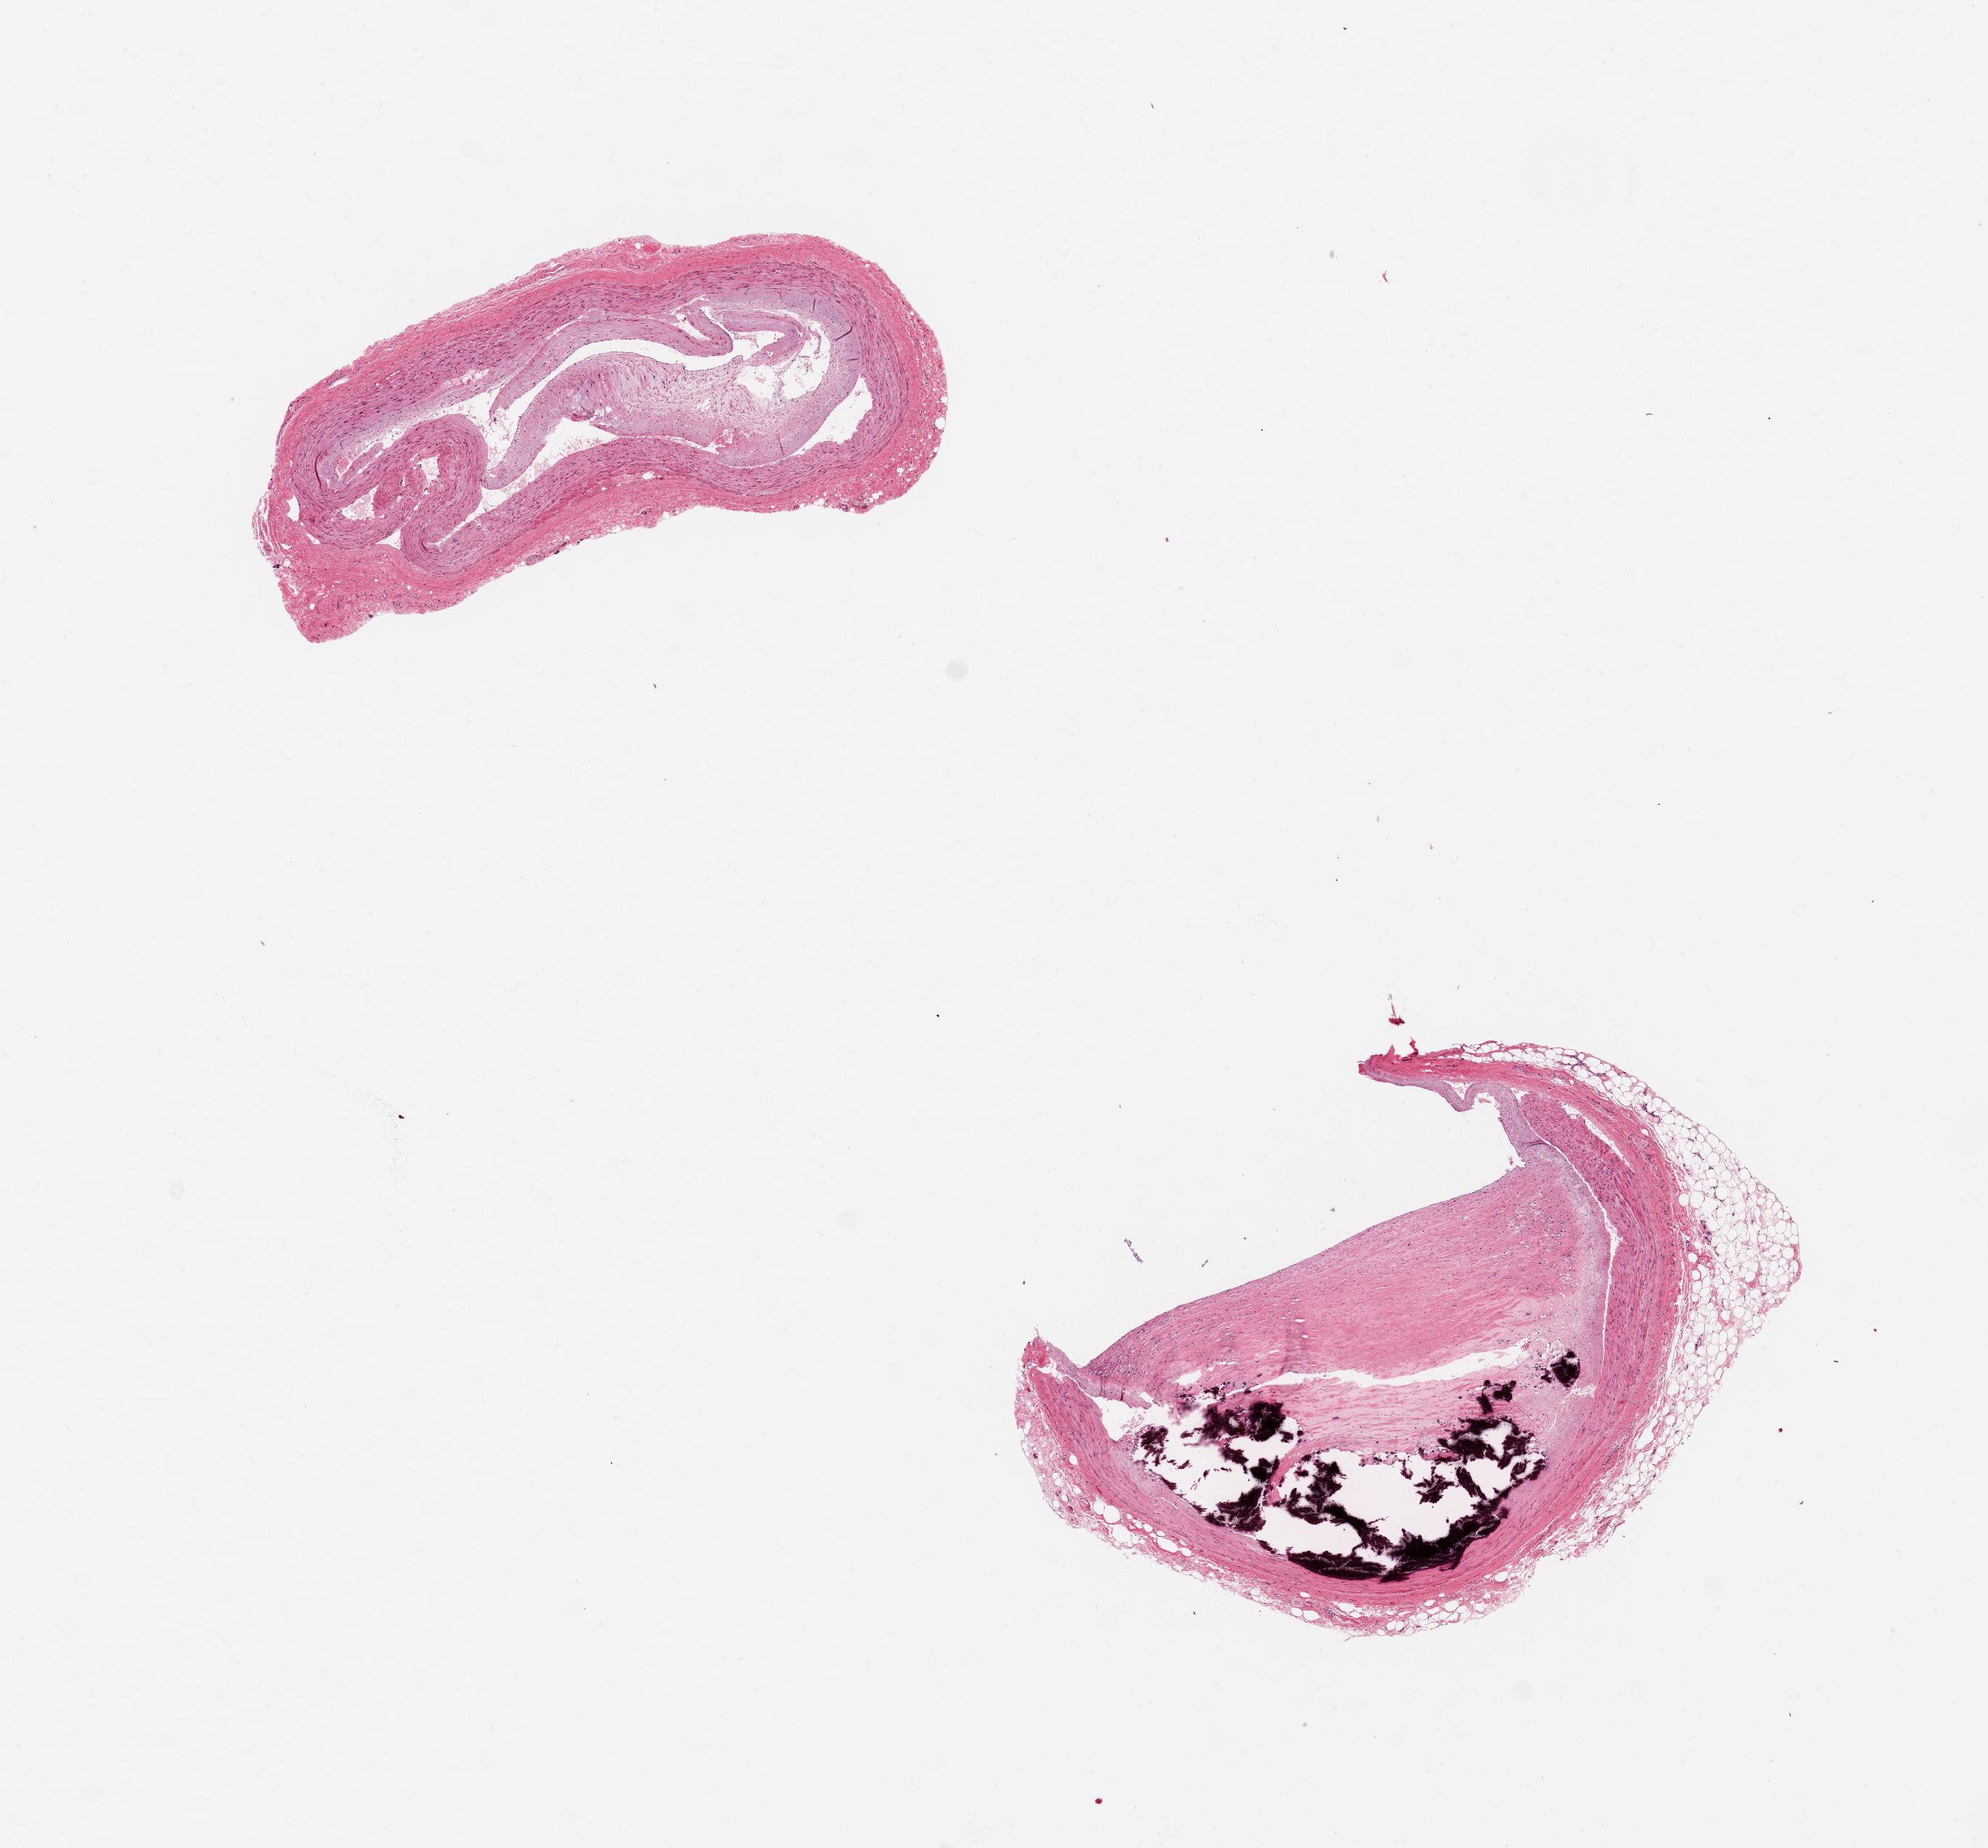
Digitized H&E-stained section — shown as a low-resolution overview of the whole scanned area (about 10.8 x 10.1 mm). PAXgene-fixed, paraffin-embedded tissue. Target tissue: coronary artery. Donor tissue sample.
Review note (as recorded): 2 pieces, 4x3 & 4x2mm. Sclerotic. calcified. one >60% occluded by plaque.